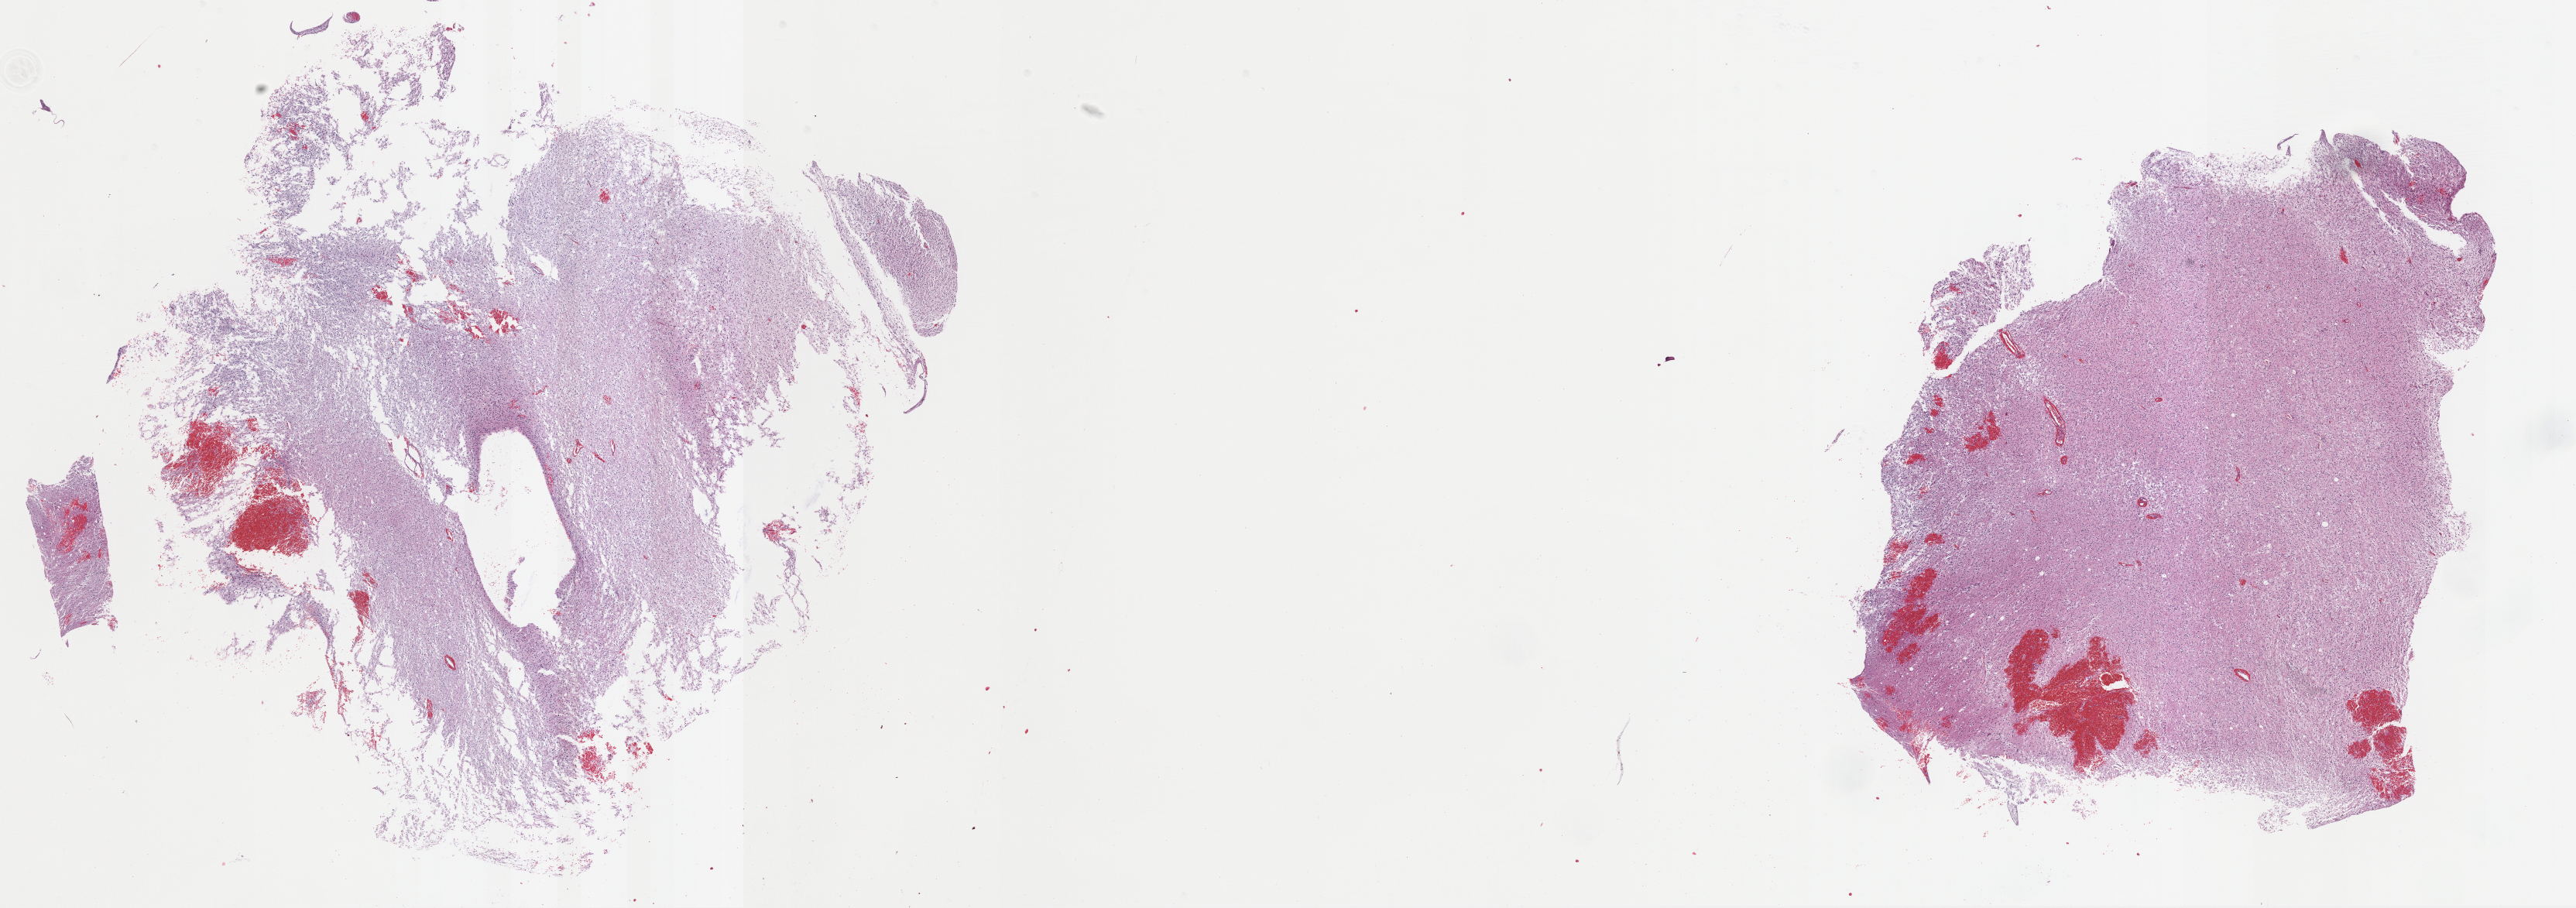
Digitized Hematoxylin and eosin (H&E) stained tissue section (whole slide) — low-resolution overview of the scanned area, about 26.8 x 9.5 mm, formalin-fixed paraffin-embedded (FFPE) diagnostic section, primary tumour sample from the brain. Male patient; age at initial diagnosis 30 years. Histologic grade: G3 (poorly differentiated).
* pathologic diagnosis: Oligodendroglioma, anaplastic